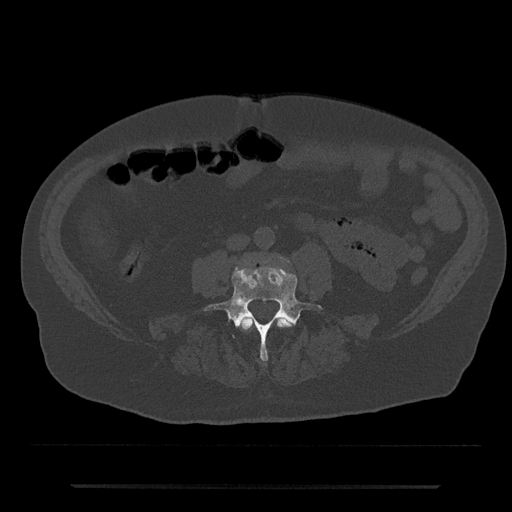
CT including the spine, one axial slice; position 362 of 797 along the scan axis; reconstruction kernel Br40s/3; bone window (W 1800 / L 400 HU); 0.5 mm slice thickness; 512 × 512 image matrix. Patient: male, 80 years. Case-level facts recorded for this patient, not image findings: primary cancer: prostate; vertebrae with lytic lesions (as recorded): L1, T11.
Outlined on this slice (semi-automatic segmentation, software-assisted and operator-edited):
- L3 vertebra: bounding box [x1, y1, x2, y2] px = [240, 317, 292, 331]
- L4 vertebra: [204, 266, 322, 361]